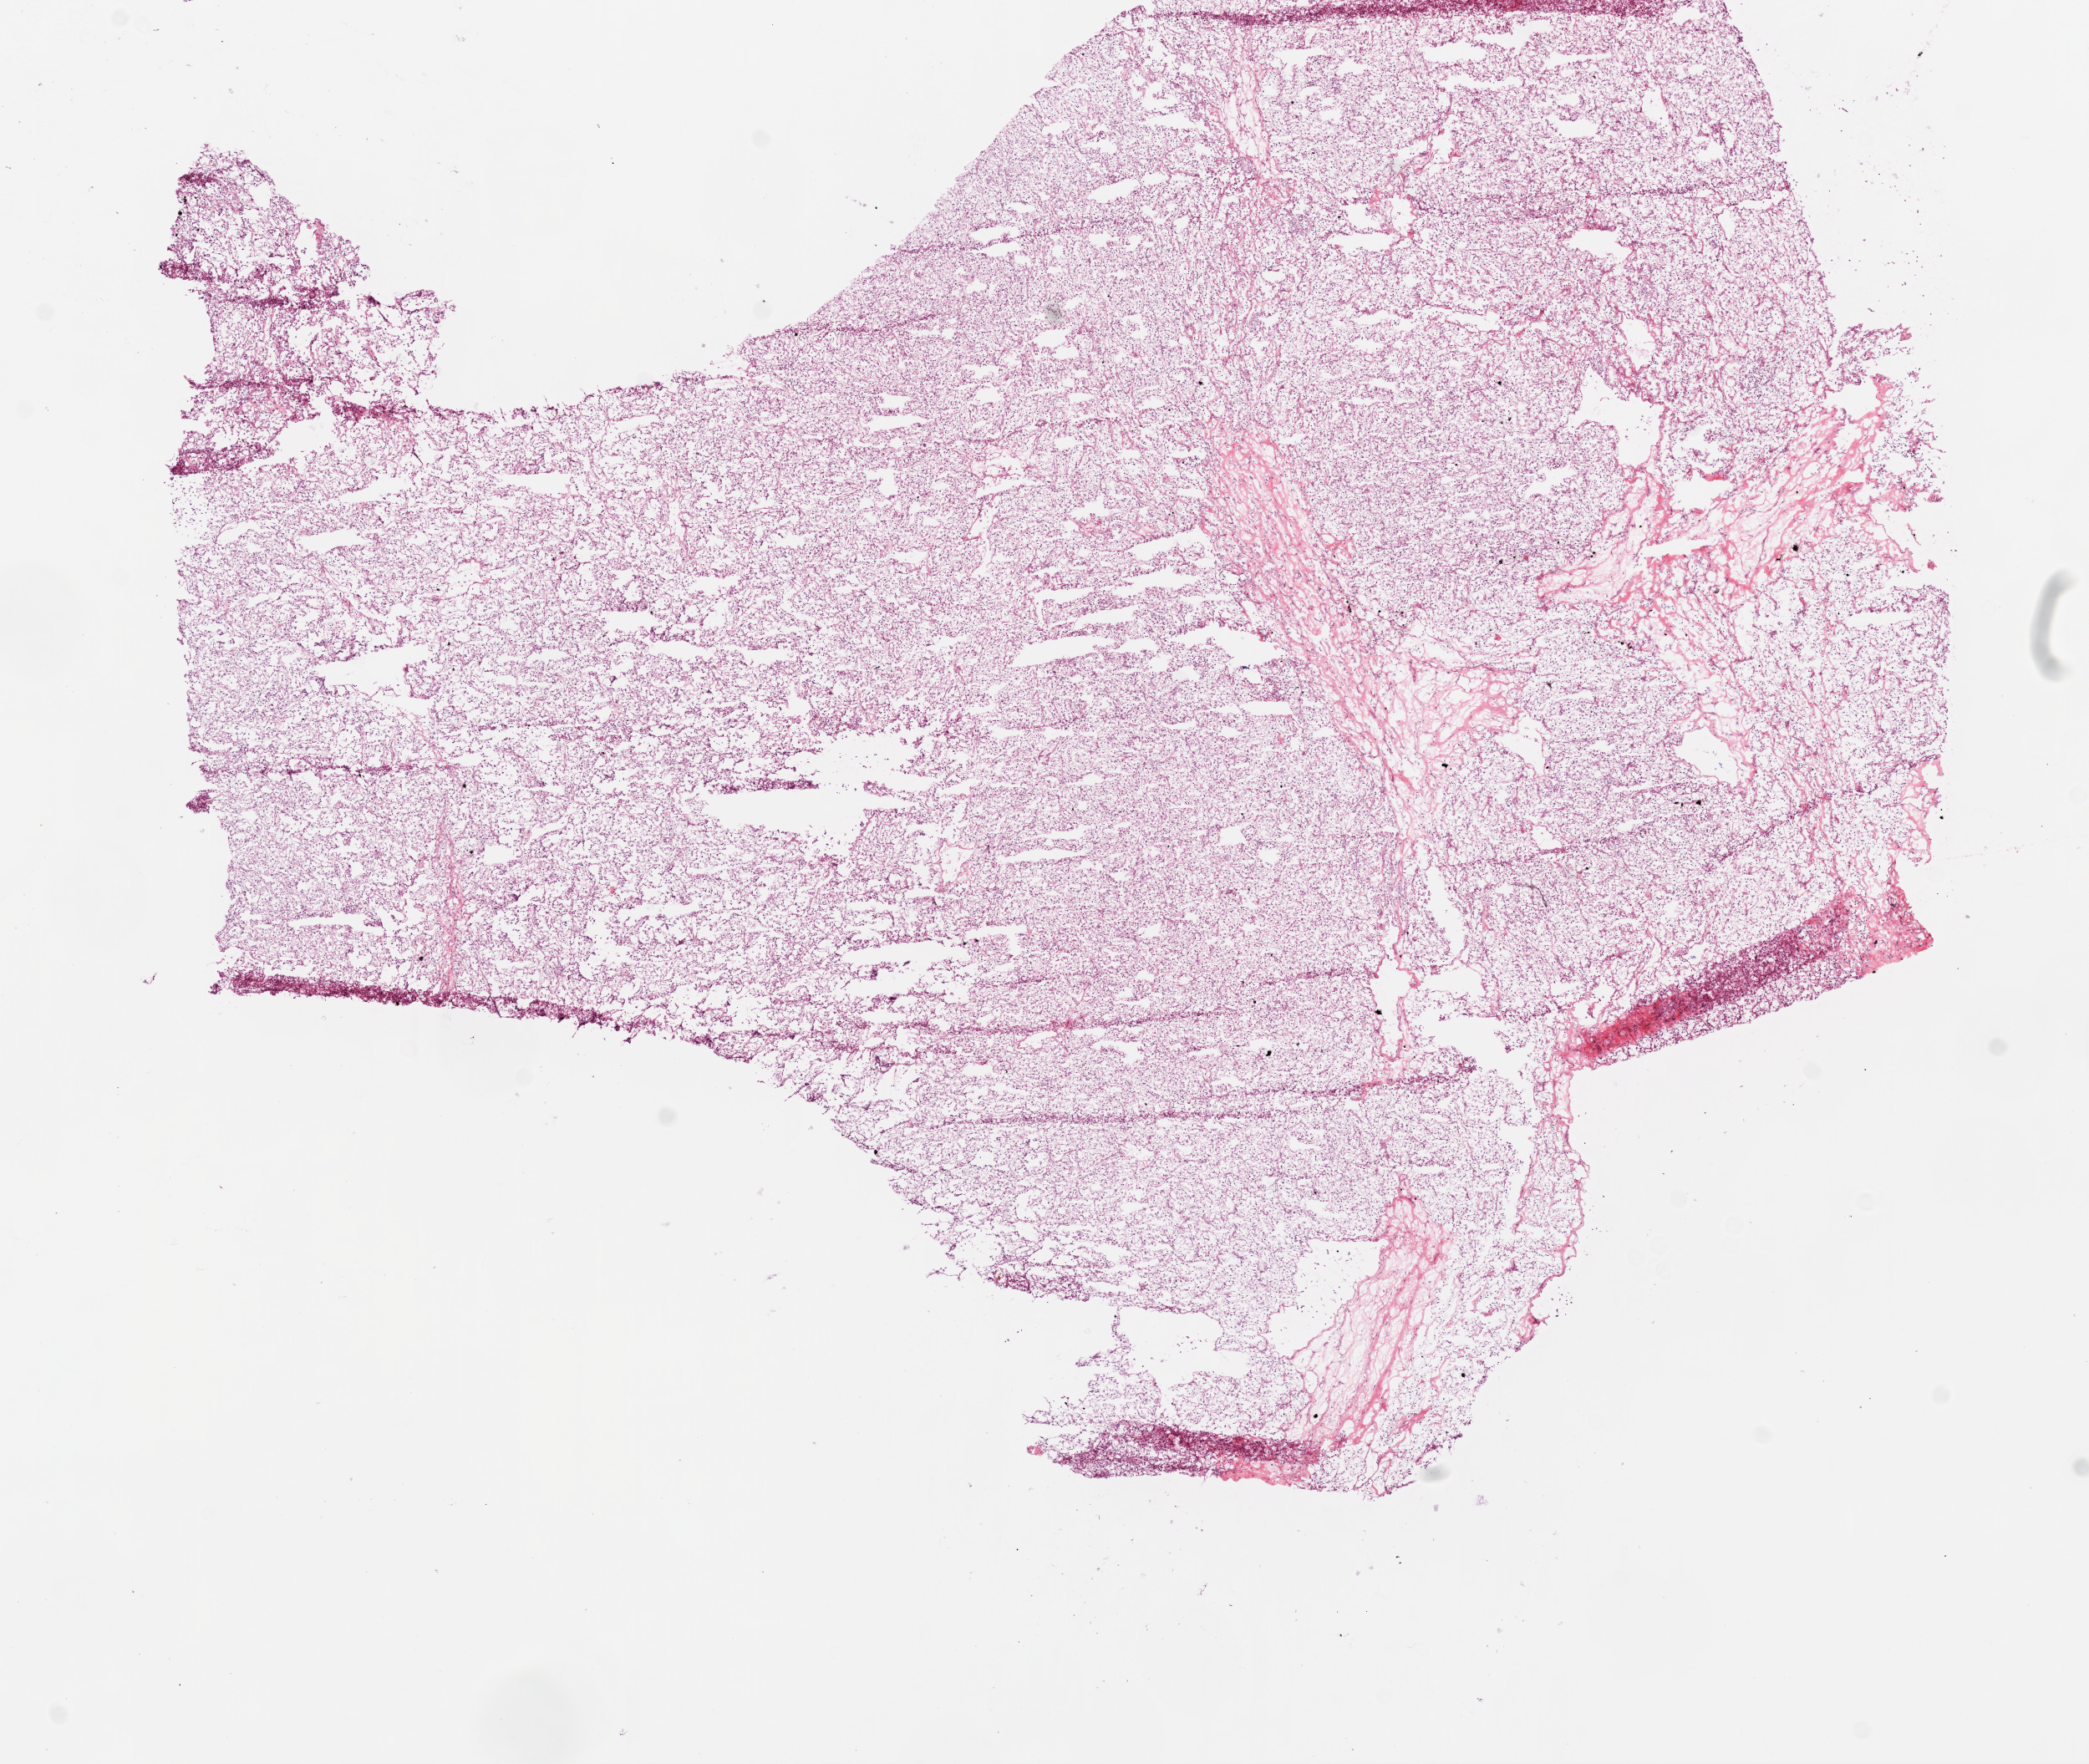
H&E-stained whole-slide image — low-resolution overview of the scanned area, about 10.0 x 8.5 mm (from a 20x scan); frozen section; primary tumour sample from the kidney. Patient: male, age at initial diagnosis 57 years. Histologic grade: G3 (poorly differentiated). Composition of this section per pathologist review: tumour cells 90%, tumour nuclei 85%, normal cells 0%, stromal cells 10%, necrosis 0%.
Laterality: left. AJCC pathologic stage: IV (7th edition). Diagnosis: Clear cell adenocarcinoma, NOS.